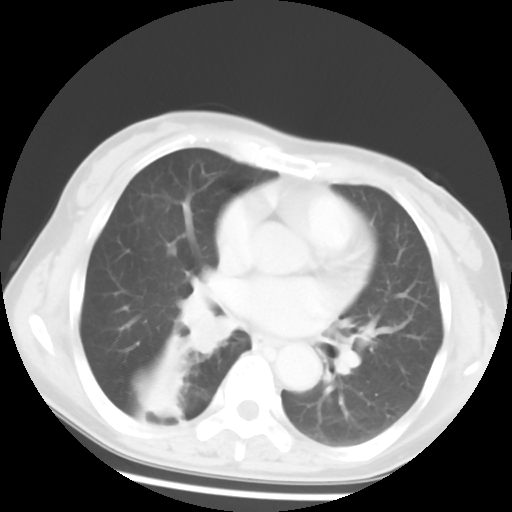
Chest CT, one axial slice; position 28 of 52 along the scan axis; reconstruction kernel STANDARD; 120 kVp; lung window (W 1500 / L -600 HU); 5 mm slice thickness; 512 × 512 image matrix, field of view 297 × 297 mm. Female patient, age 54 years. Case-level facts recorded for this patient, not image findings: clinical TNM (as recorded): T1c N0 M0; histopathological grade: G1-2.
Annotated regions visible in this slice (bounding box drawn by a radiologist):
- lung tumour (recorded histology: squamous cell carcinoma): bounding box (x1, y1, x2, y2) in pixels: (169, 278, 234, 362)